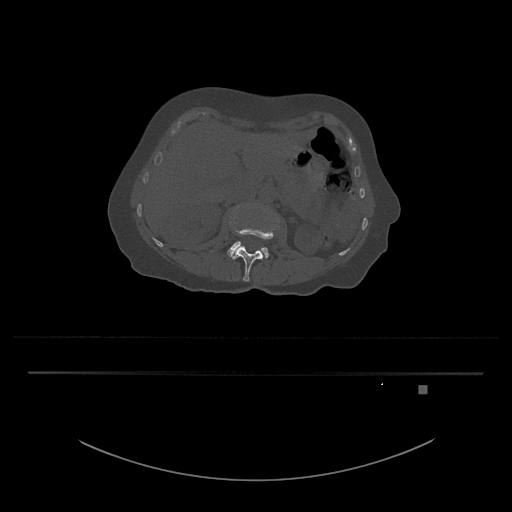
CT including the spine, one axial slice; slice 472 of 797 in the series (ordered by position); bone window (W 1800 / L 400 HU); 0.5 mm slice thickness; 512 × 512 image matrix. Female patient, age 57 years. From the clinical record (not read from this slice): primary cancer: cervical.
Outlined on this slice (semi-automatic segmentation, software-assisted and operator-edited):
- L3 vertebra: bounding box [x1, y1, x2, y2] px = [227, 206, 269, 259]